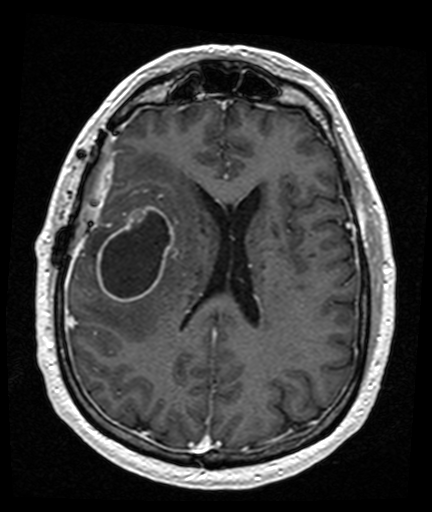
Brain MRI from a brain-tumour surgery series, one axial slice. Slice 66 of 176 in the series (ordered by position). T1-weighted post-contrast. 1 mm slice thickness. 432 × 512 image matrix, field of view 194 × 230 mm. Case-level facts recorded for this patient, not image findings: histopathology: Glioblastoma; WHO grade: 4; IDH mutation: no; tumour location: Right Frontal Temporal, Posterior Sylvian Fissure.
Annotated regions visible in this slice (outlined manually by an expert reader):
- tumour: bounding box (x1, y1, x2, y2) in pixels: (97, 205, 175, 302)